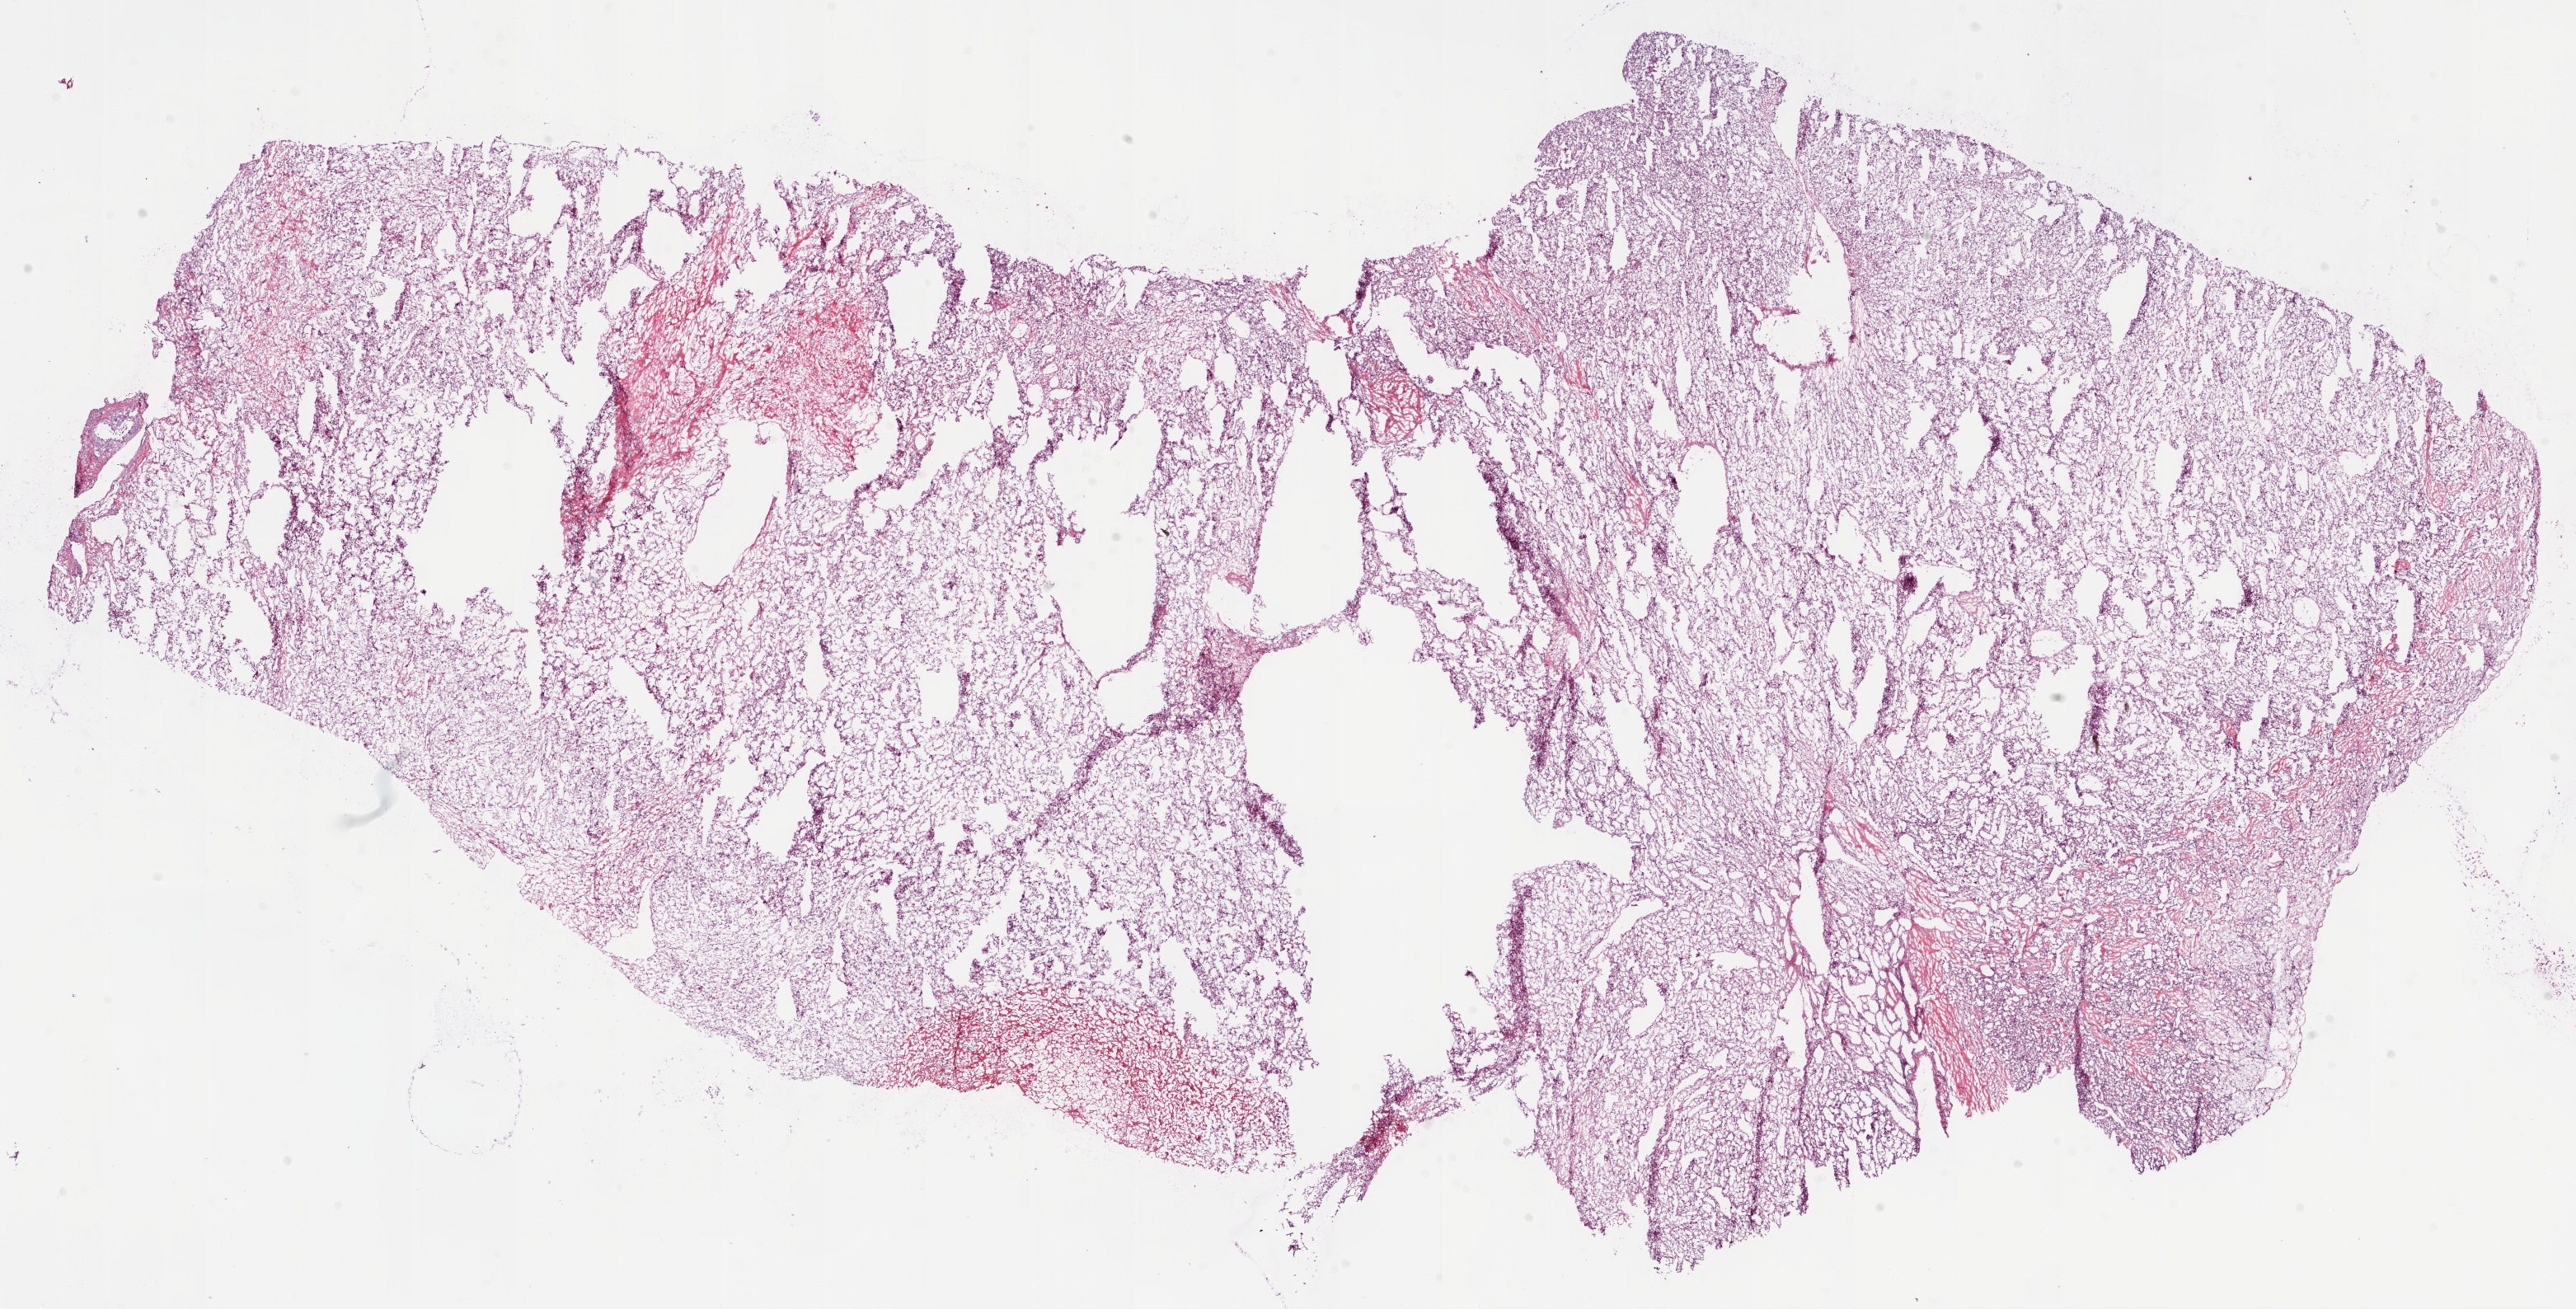
Digitized Hematoxylin and eosin (H&E) stained tissue section (whole slide) — shown as a low-resolution overview of the whole scanned area (about 25.1 x 12.7 mm), frozen section from the bottom of the tissue portion, primary tumour sample from the kidney. Male patient; age at initial diagnosis 78 years. Histologic grade: G4 (undifferentiated). Pathologist review of this section (percent, as recorded): tumour cells 90%, tumour nuclei 90%, normal cells 0%, stromal cells 10%, necrosis 0%.
Diagnosis: Clear cell adenocarcinoma, NOS. AJCC pathologic stage: II. Laterality: right.